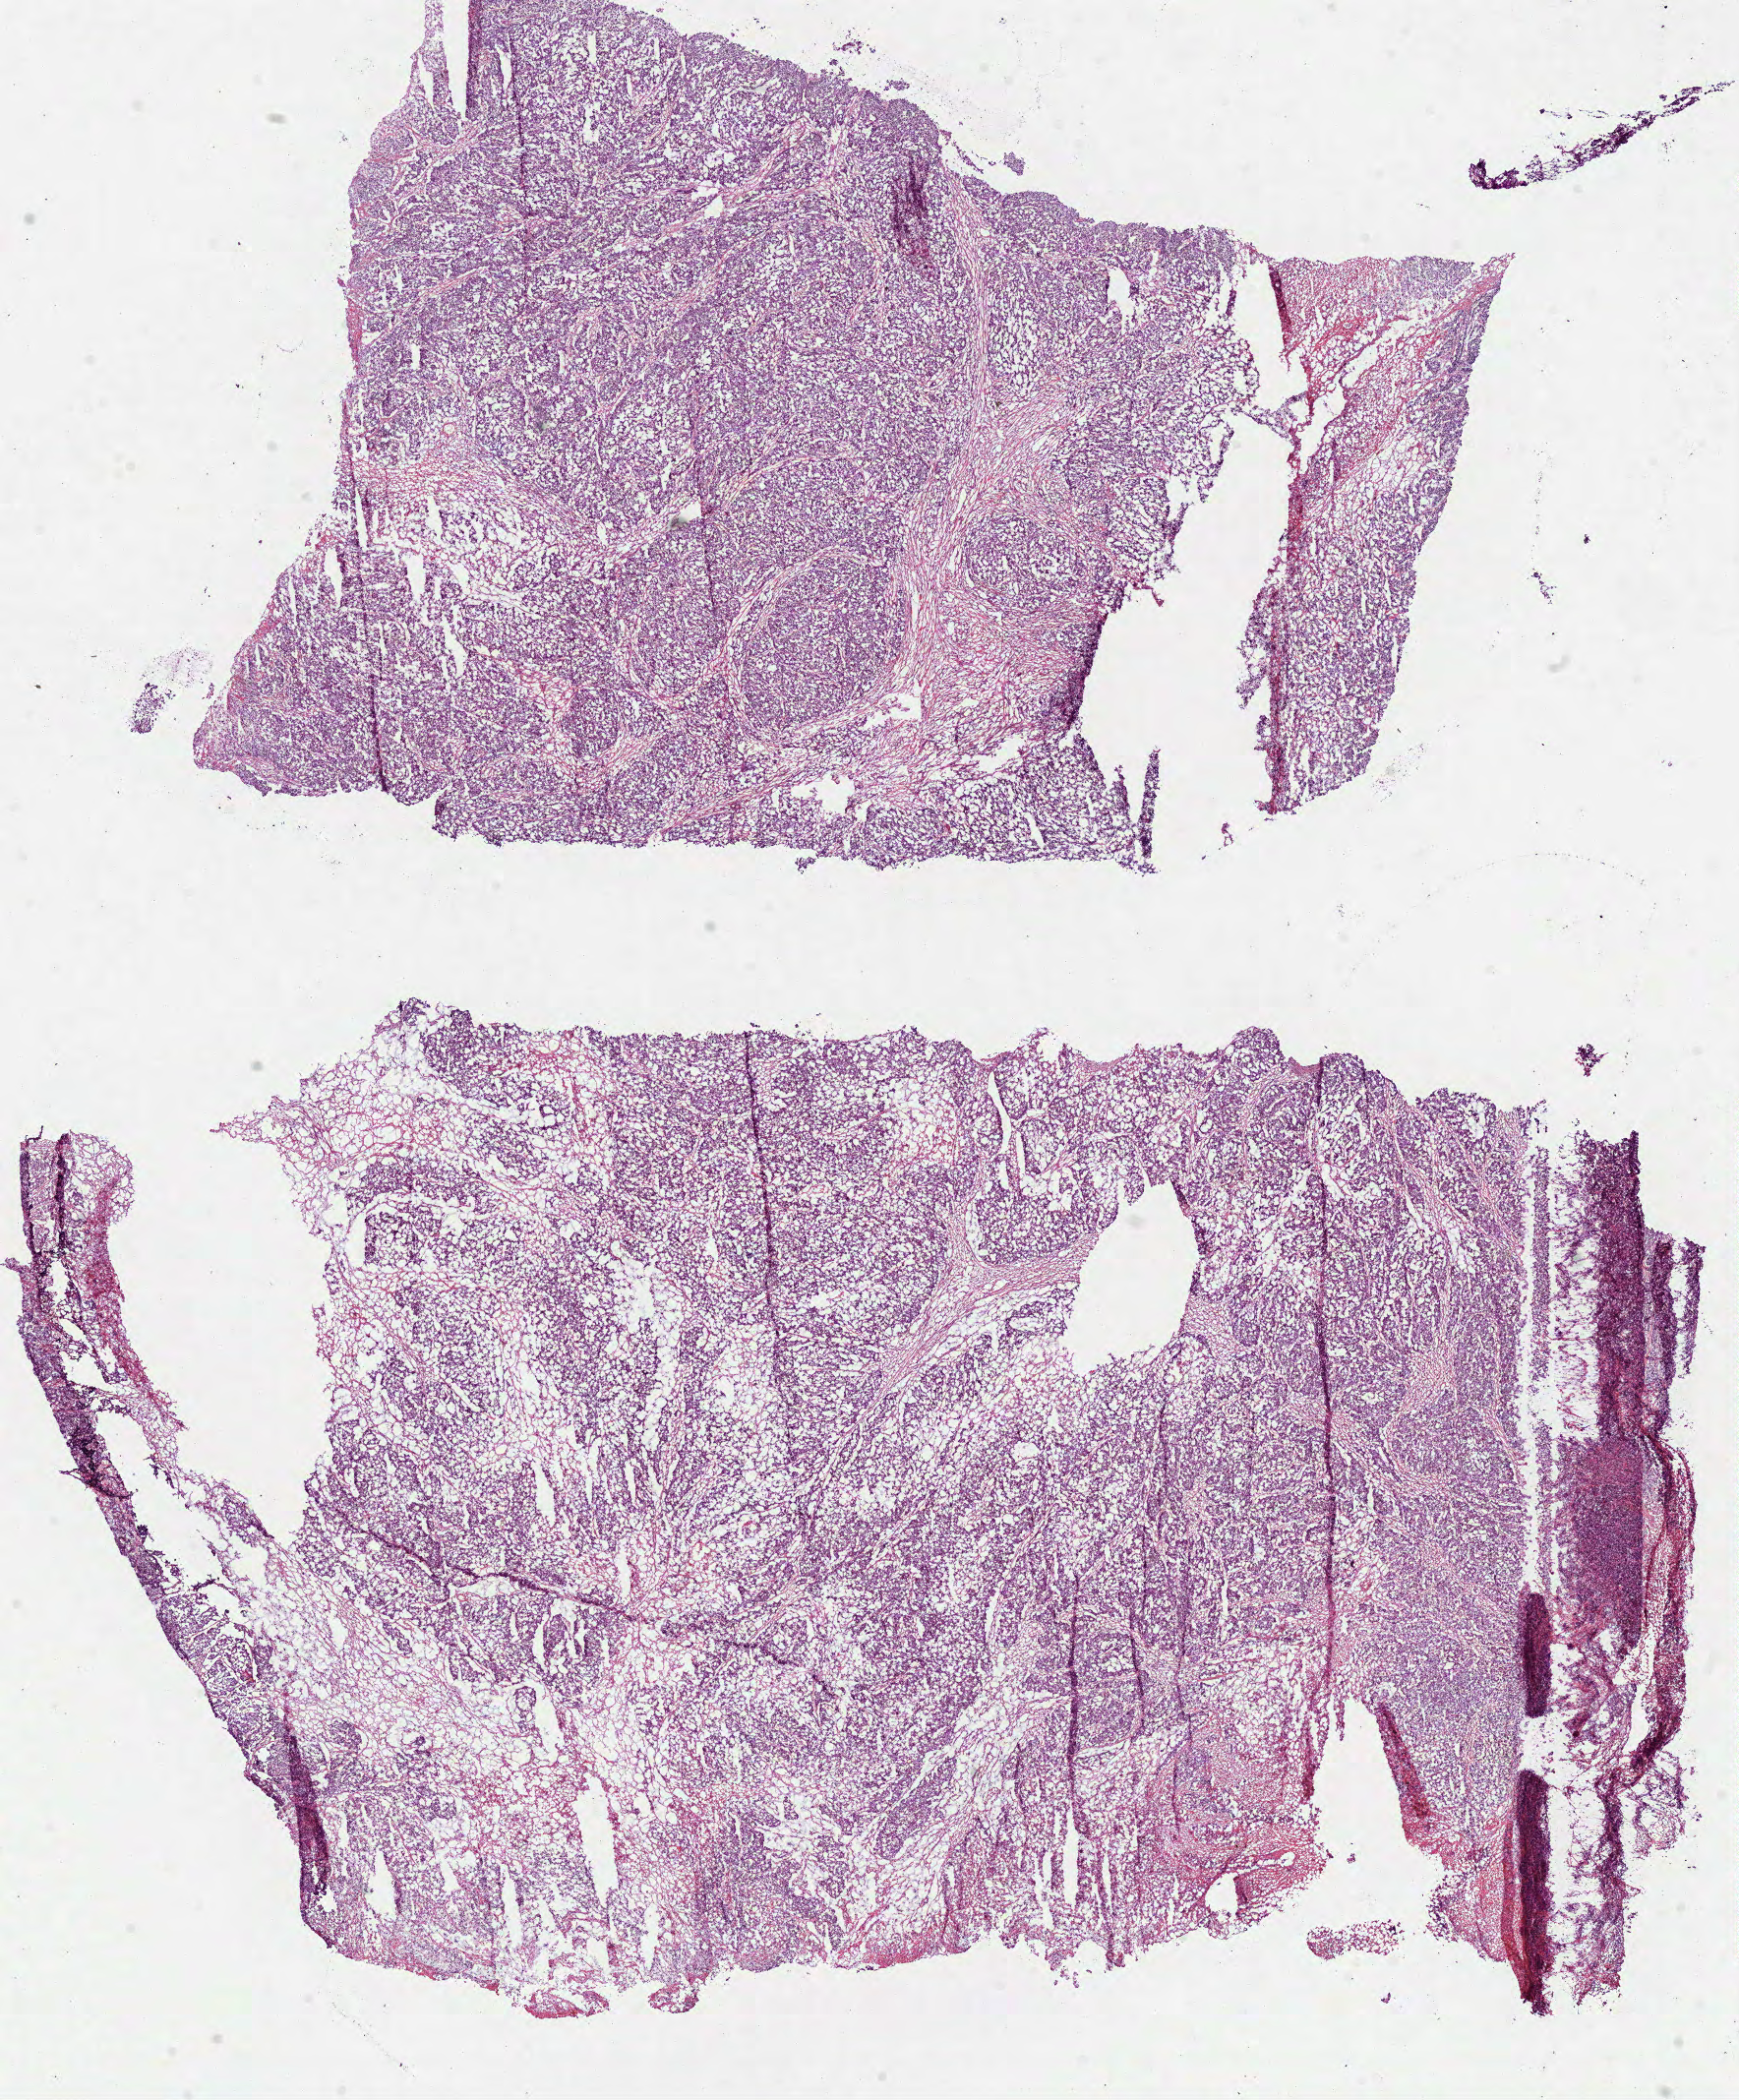
Digitized H&E tissue section (whole slide) — low-resolution overview of the scanned area, about 14.3 x 17.2 mm (slide scanned at 40x). Frozen section. Primary tumour sample from the colon. Female, age 77 years at initial diagnosis. Composition of this section per pathologist review: tumour cells 85%, tumour nuclei 80%, normal cells 0%, stromal cells 10%, necrosis 5%.
Pathologic diagnosis: Adenocarcinoma, NOS. AJCC pathologic stage: II (5th edition). TNM: T3 N0 MX. Lymph nodes positive (case pathology): 0 of 24 examined.